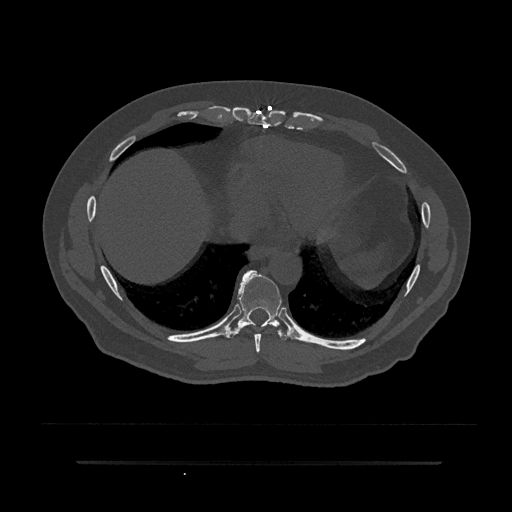
CT including the spine, one axial slice; slice 395 of 797 in the series (ordered by position); bone window (W 1800 / L 400 HU); 0.5 mm slice thickness; 512 × 512 image matrix. Patient: male, 59 years. Case-level facts recorded for this patient, not image findings: primary cancer: bile ducts.
Annotated regions visible in this slice (semi-automatically segmented with operator editing):
- T8 vertebra: bounding box [x1, y1, x2, y2] px = [254, 333, 261, 353]
- T9 vertebra: [227, 270, 289, 340]